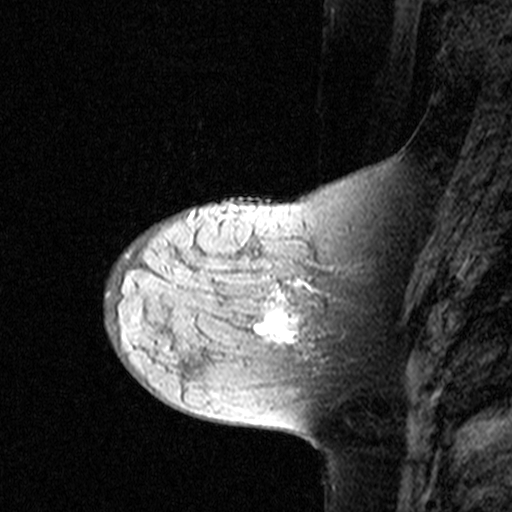
Breast MRI (dynamic contrast-enhanced), one sagittal slice. Position 12 of 44 along the scan axis. Dynamic contrast-enhanced study with each time point stored as its own series, time point 2 of 3 at this slice position (early post-contrast, ordered by acquisition time). 1.5 T. TE 4.5 ms, TR 11 ms. 512 × 512 image matrix, field of view 200 × 200 mm. Patient: female, 44 years. From the clinical record (not read from this slice): setting: breast cancer imaged before/during neoadjuvant chemotherapy; receptor status: triple-negative.
Annotated regions visible in this slice (semi-automatically segmented with operator editing):
- analysis volume of interest (the breast-tissue region the enhancement analysis was run in; not a lesion): bounding box [x1, y1, x2, y2] px = [142, 208, 349, 363]
- tumour enhancement mask (voxels above the 90 % enhancement threshold inside the analysis volume of interest): [265, 284, 302, 344]